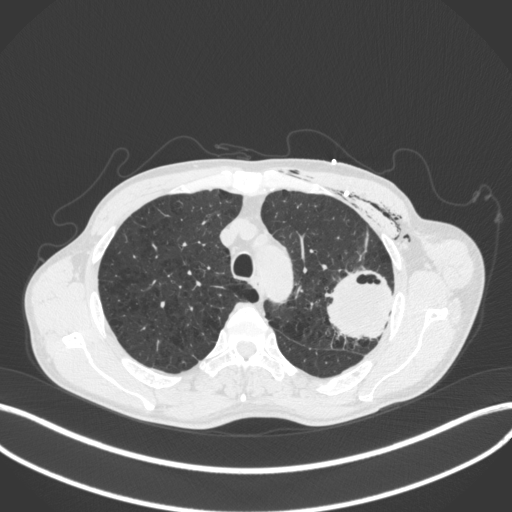
Chest CT, one axial slice; slice 308 of 416 in the series (ordered by position); reconstruction kernel B31f; 120 kVp; lung window (W 1500 / L -600 HU); 512 × 512 image matrix, field of view 400 × 400 mm. Male patient, age 58 years. Case-level facts recorded for this patient, not image findings: clinical TNM (as recorded): T3 N0 M0.
Annotated regions visible in this slice (bounding box drawn by a radiologist):
- lung tumour (recorded histology: adenocarcinoma): bounding box (x1, y1, x2, y2) in pixels: (324, 271, 396, 339)